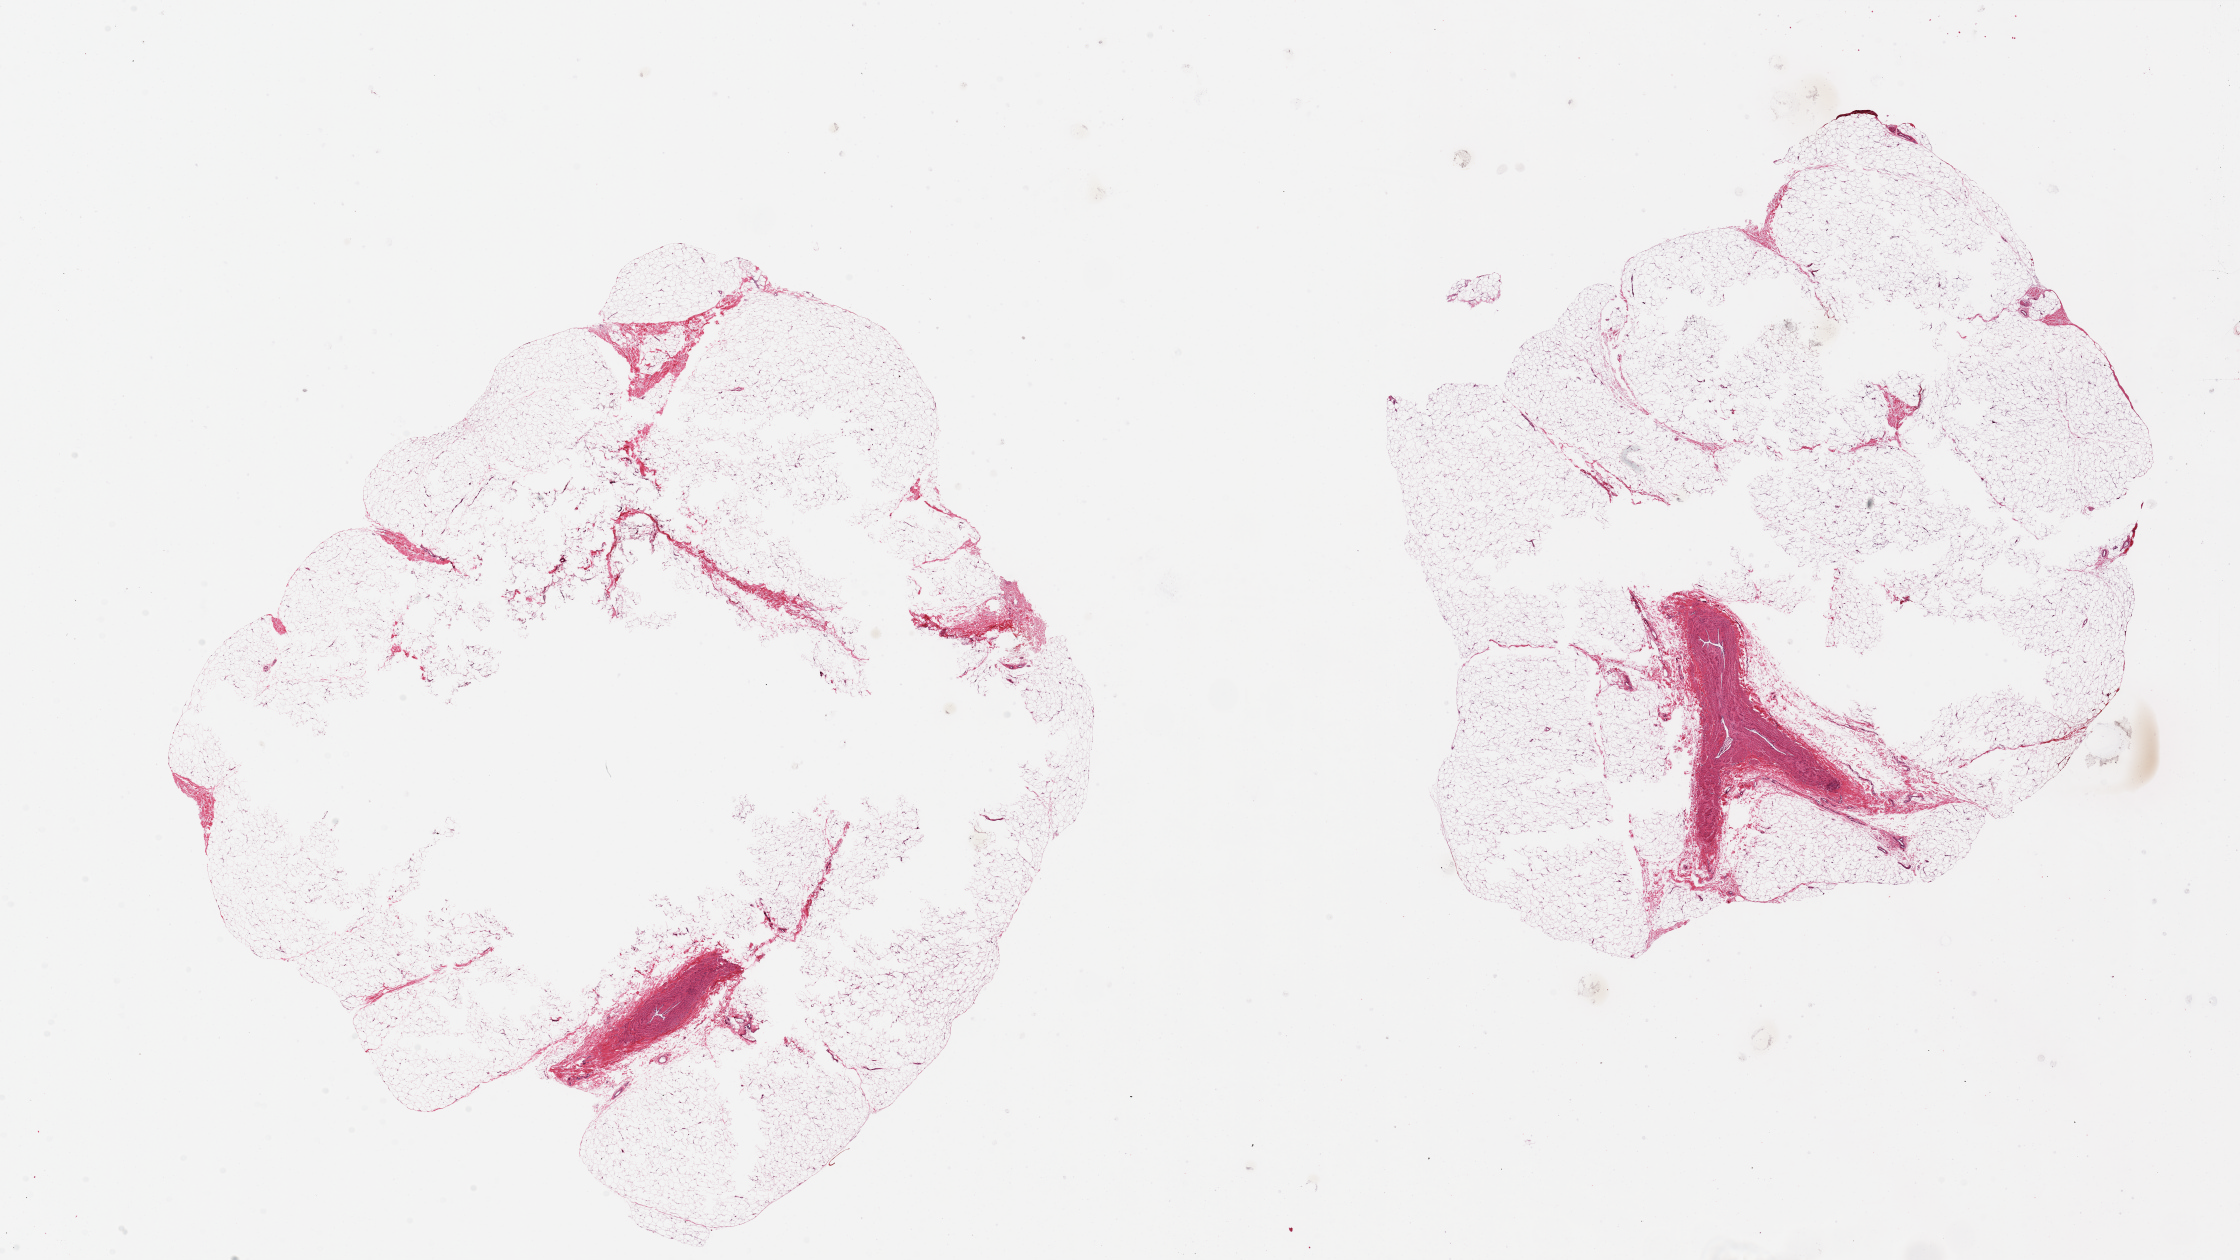
Digitized hematoxylin and eosin (H&E)-stained section, a low-resolution overview of the entire scanned area, about 35.4 x 19.9 mm, PAXgene-fixed paraffin-embedded (PFPE) section, sampled site (target tissue): adipose tissue, tissue donor sample.
Reviewer comment on this tissue sample: 2 pieces 16x14 & 14x12 mm; aliquots are too large and have central unfixed areas. Each contains 1.5 mm blood vessels.